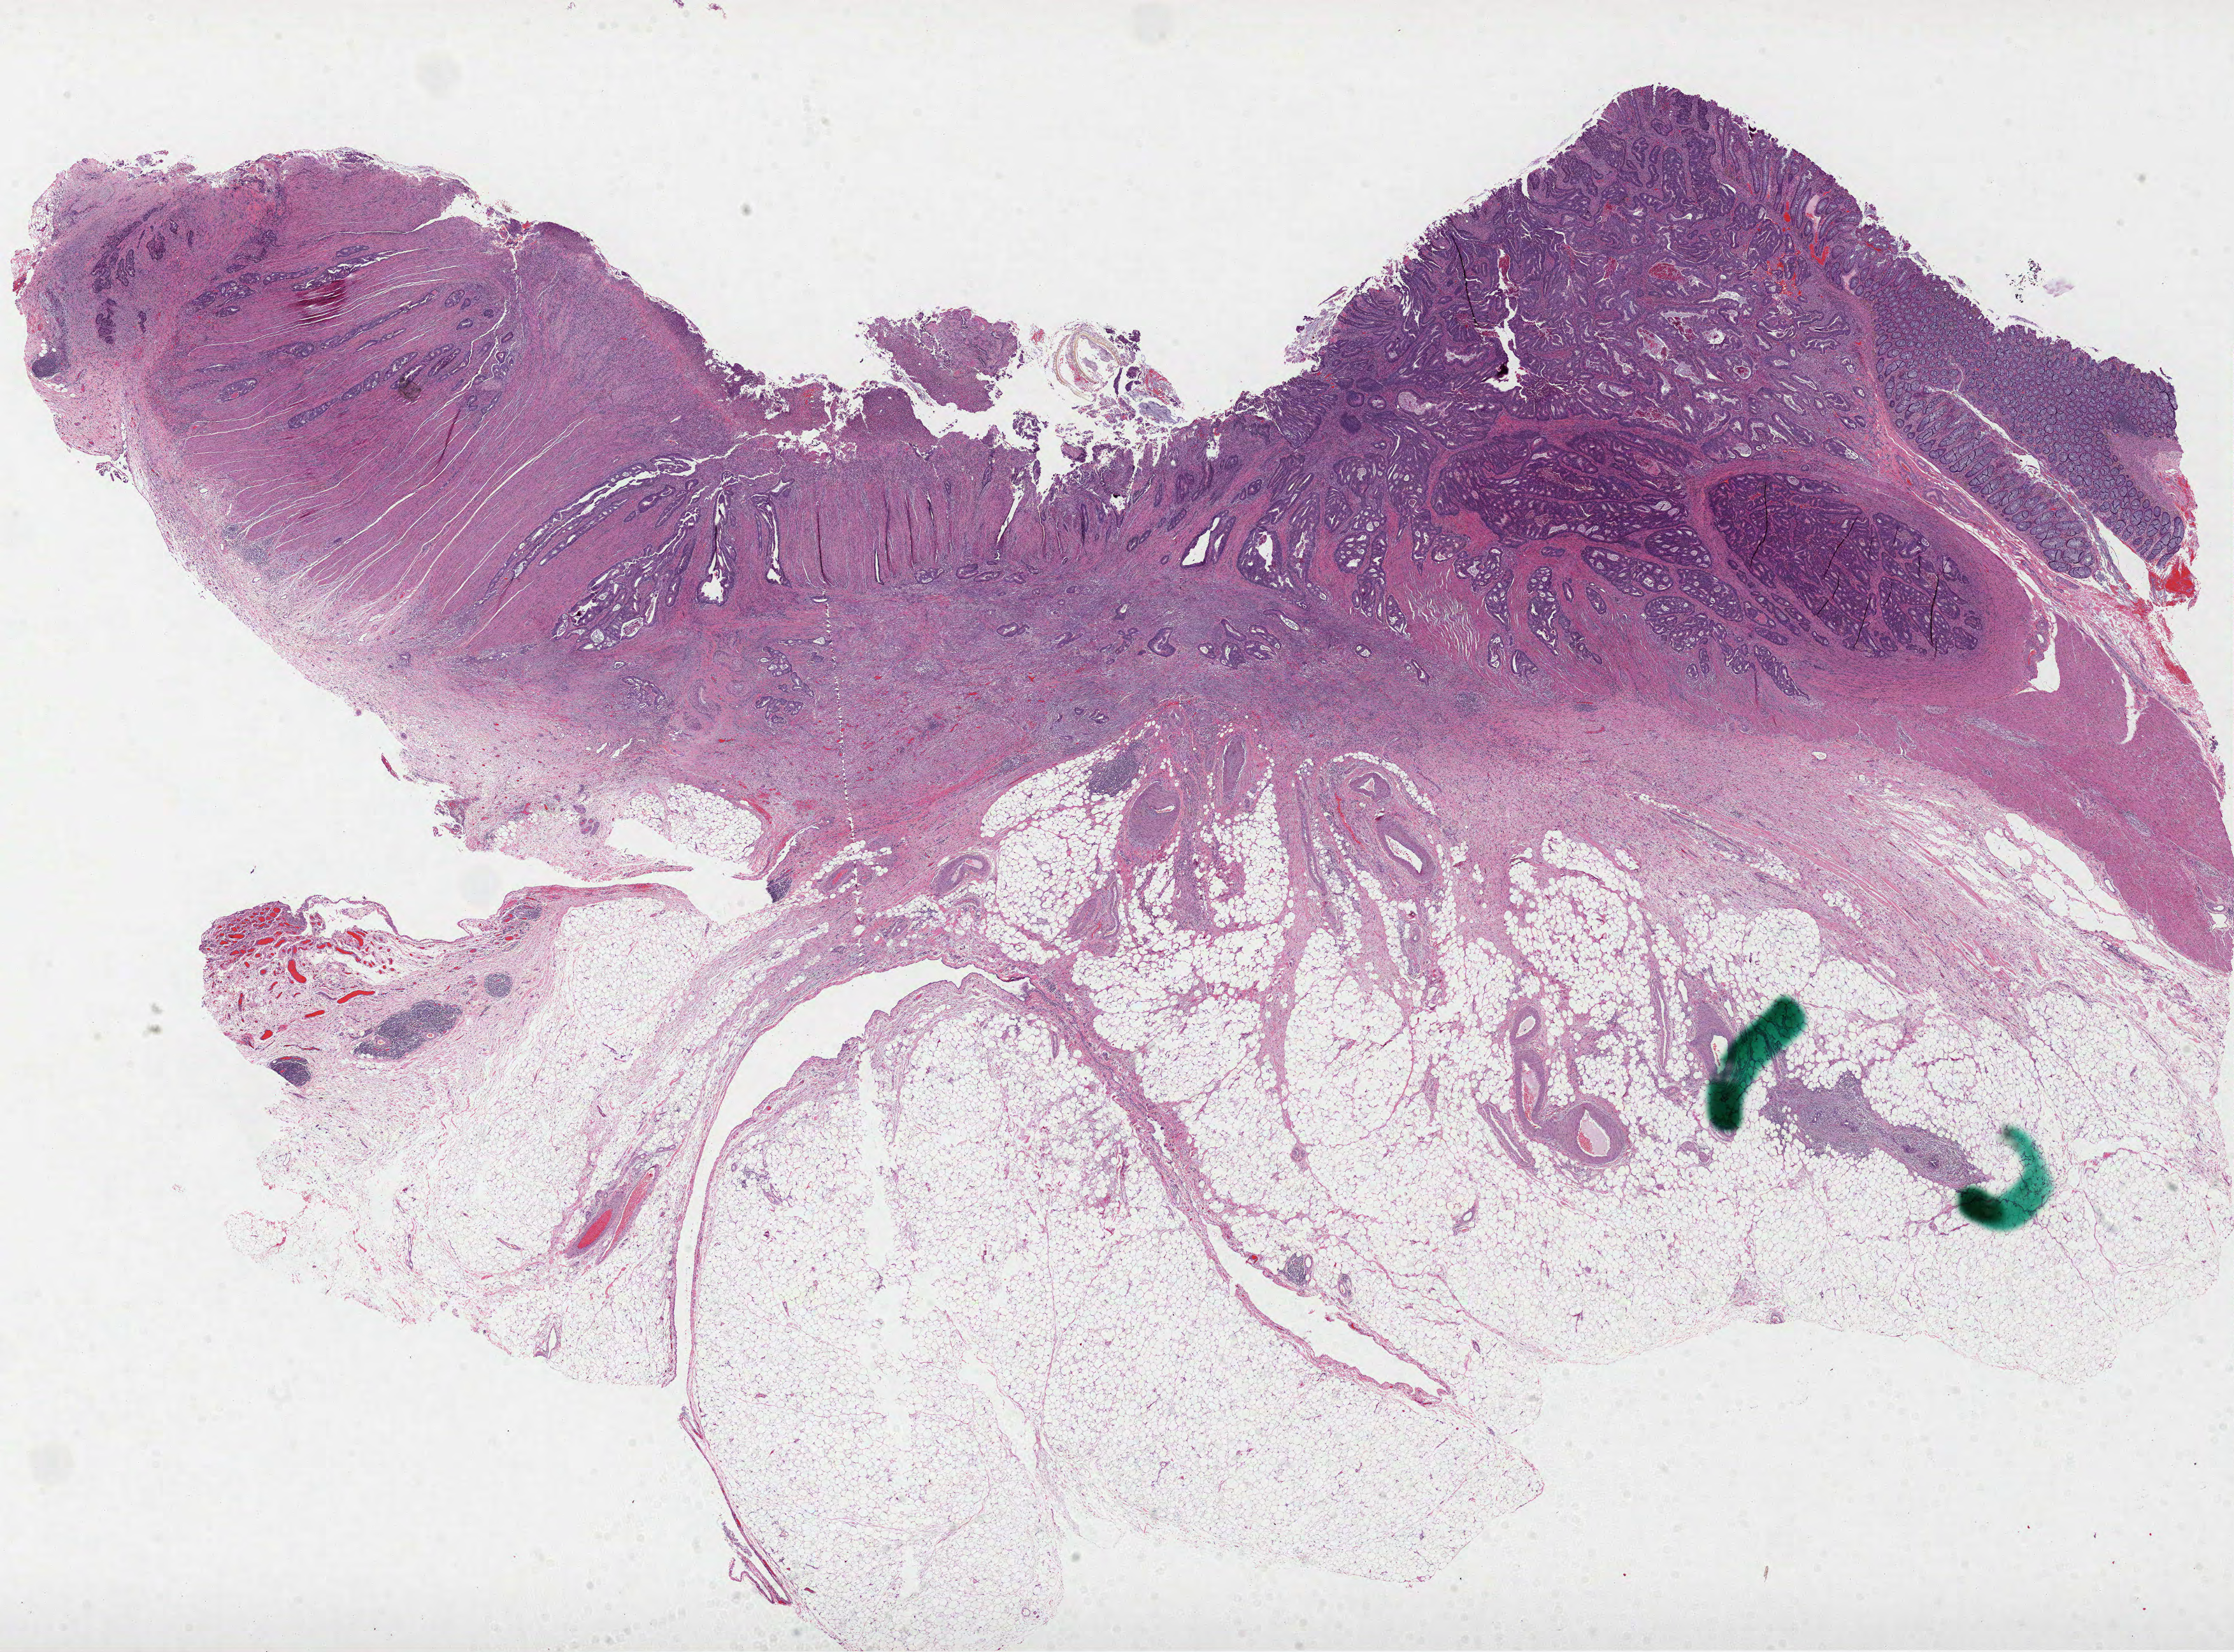
Digitized H&E tissue section (whole slide), a low-resolution overview of the entire scanned area, about 28.3 x 20.9 mm; formalin-fixed paraffin-embedded (FFPE) diagnostic section; primary tumour sample from the colon. Patient: male, age at initial diagnosis 72 years.
Lymph nodes positive (case pathology): 1 of 19 examined. AJCC pathologic stage: IIIB. Diagnosis: Adenocarcinoma, NOS (cecum).